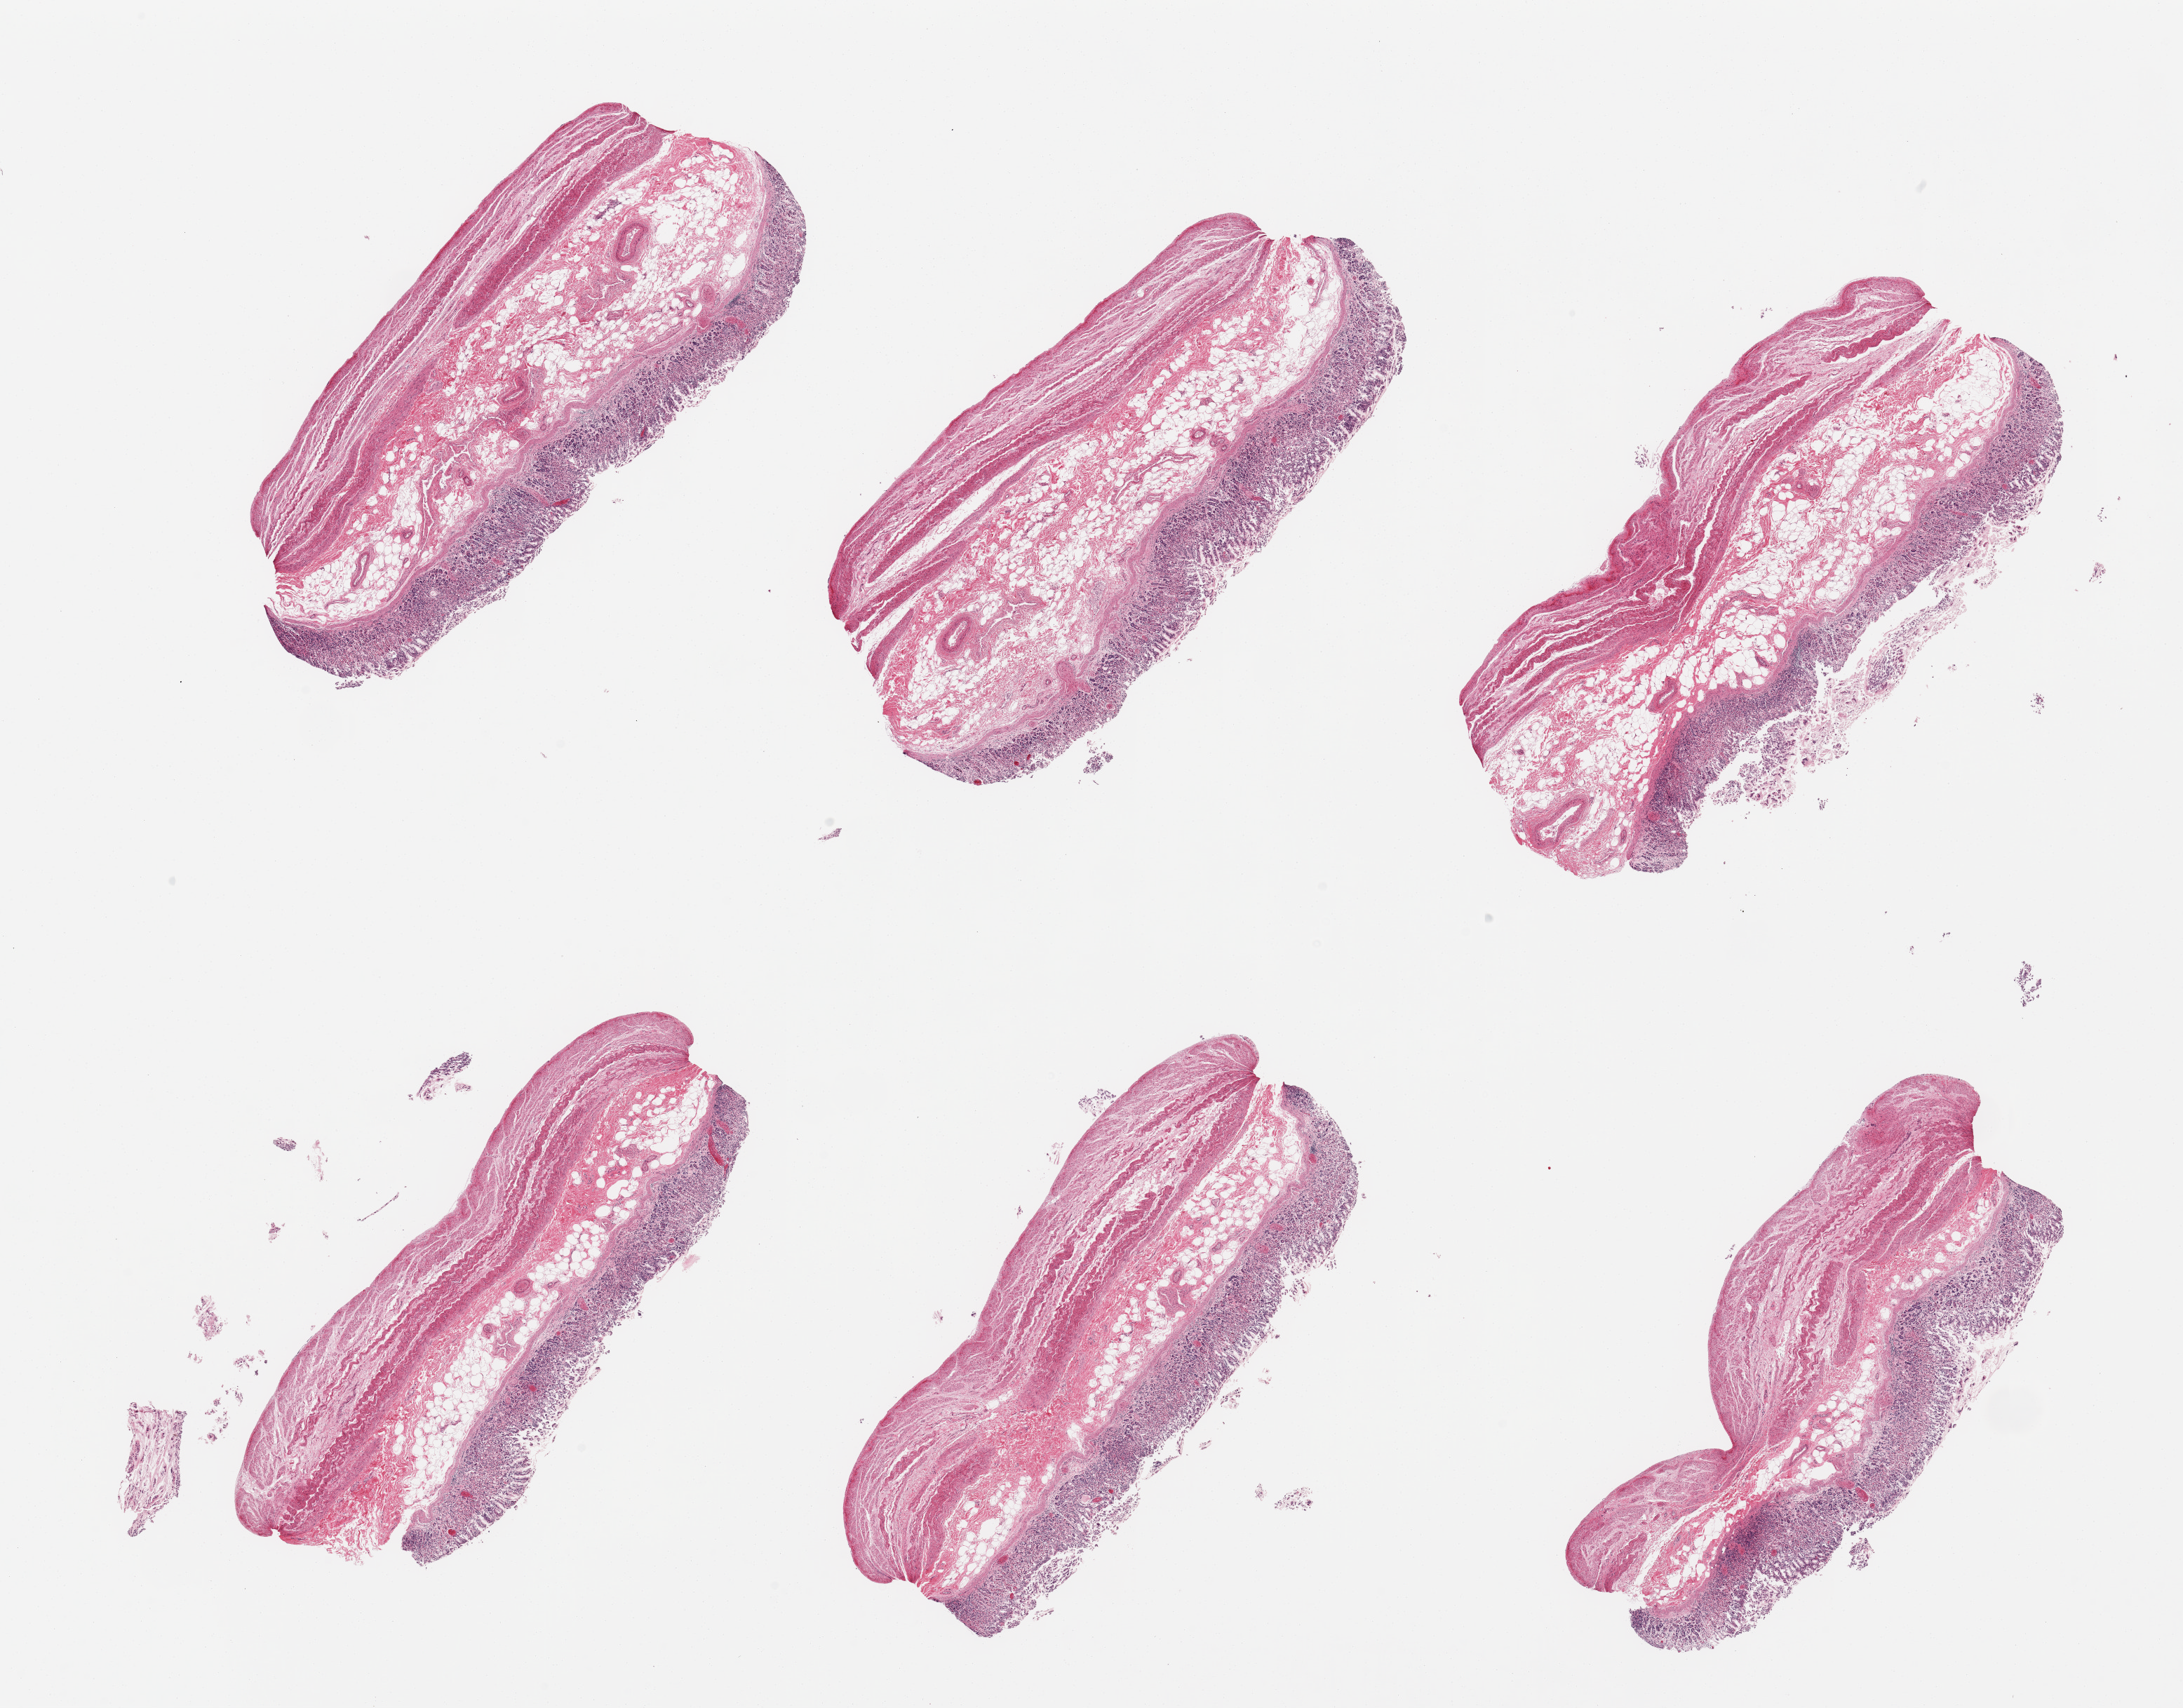
Whole-slide image, haematoxylin and eosin stain — whole scanned area (about 24.6 x 19.3 mm) shown as a low-resolution overview; PAXgene-fixed paraffin-embedded (PFPE) section; target tissue: stomach; tissue donor sample.
Reviewer comment on this tissue sample: 6 pieces, mucosa up to ~0.8mm, advanced autolysis.